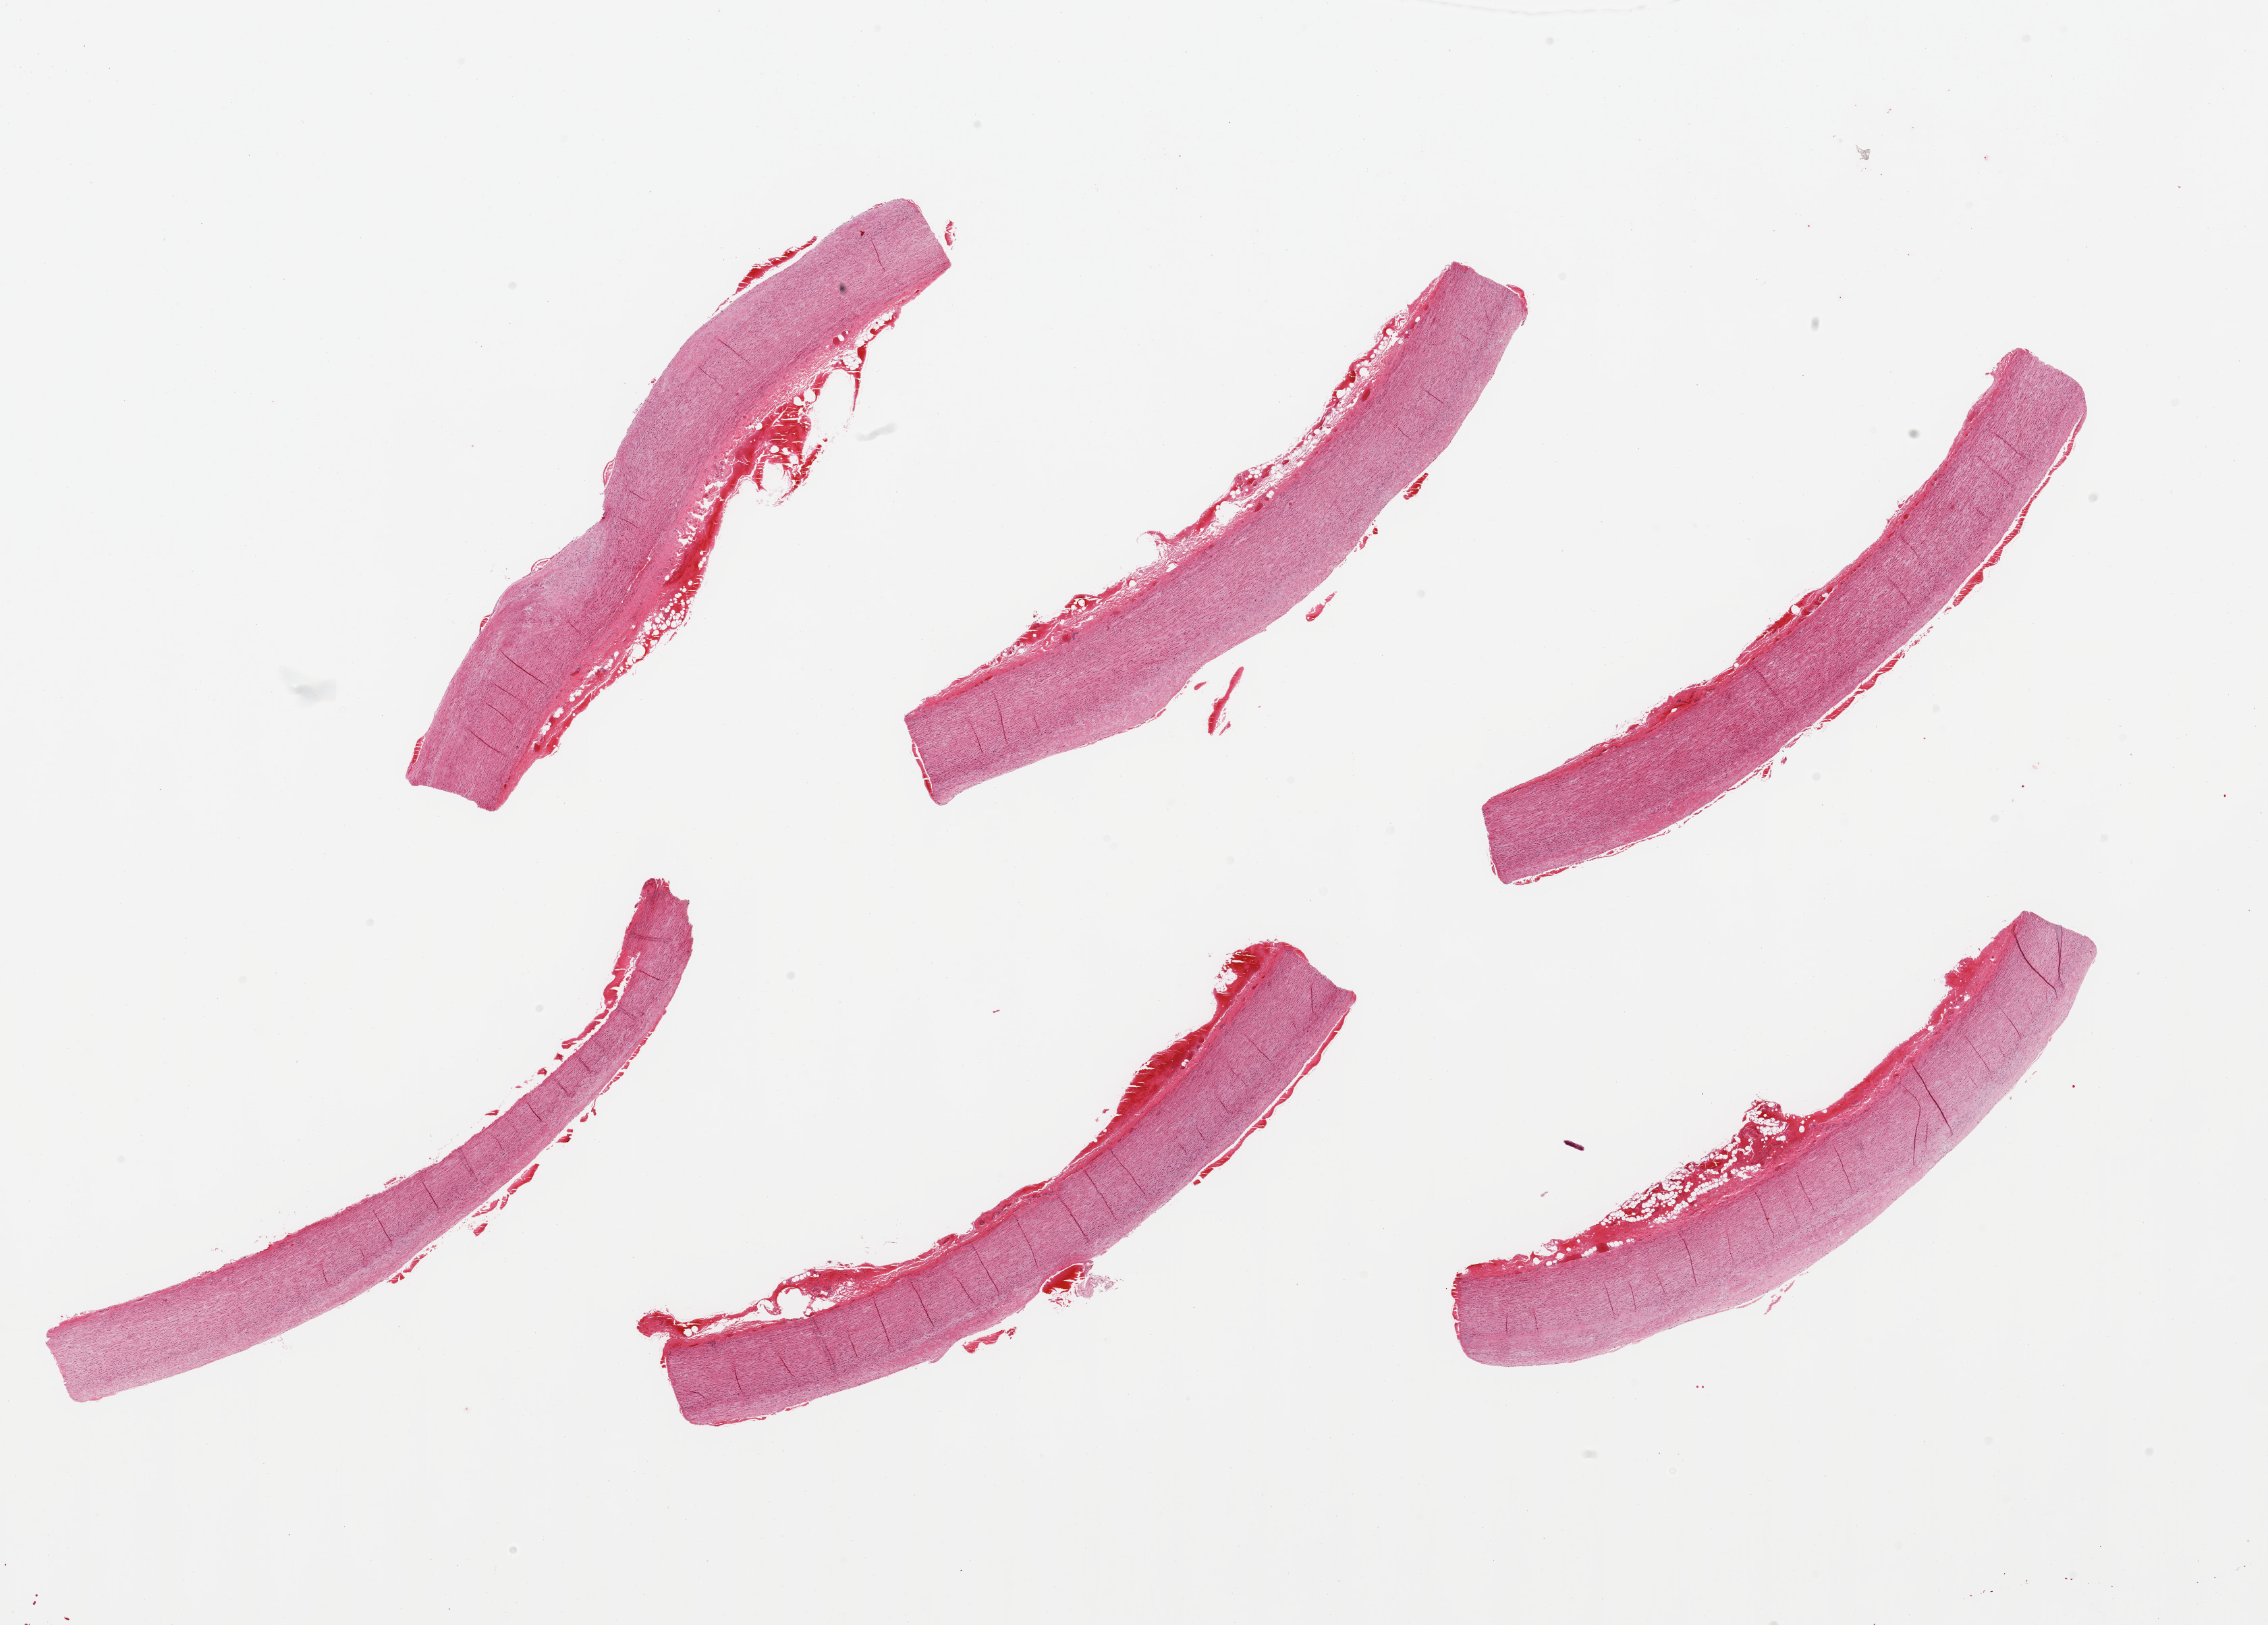
Digitized hematoxylin and eosin (H&E)-stained section — a low-resolution overview of the entire scanned area, about 26.6 x 19.0 mm; PAXgene-fixed paraffin-embedded (PFPE) section; sampled site (target tissue): aorta; tissue donor sample. Male donor.
• review note (as recorded): 6 pieces; flat plaques; recent adventitial hemorrhage